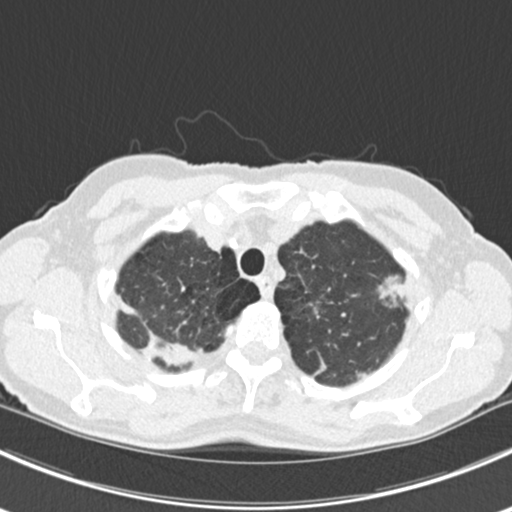
Axial slice from a low-dose chest CT screening exam, baseline screening round, lung window (W 1500 / L -600 HU), 2 mm slice thickness, slice 32 of 224 in the series, 512 × 512 image matrix, field of view 310 × 310 mm. Female participant, aged 63 years at enrolment. Current smoker at enrolment.
Expert-annotated lung lesion, box from (x=367, y=265) to (x=420, y=319) px. The screening reader recorded 10 non-calcified nodules or masses ≥4 mm on this exam; which of them this box marks is not recorded. Lung cancer was diagnosed 751 days after this screen (after the third annual screen): bronchiolo-alveolar adenocarcinoma, NOS, right upper lobe, right middle lobe, right lower lobe, left upper lobe, left lower lobe, moderately differentiated (G2), stage IV (AJCC 6th edition).